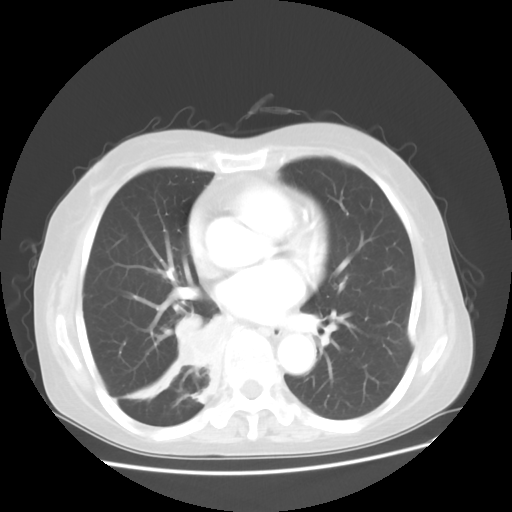
Chest CT, one axial slice. Slice 21 of 48 in the series (ordered by position). 120 kVp. Lung window (W 1500 / L -600 HU). 5 mm slice thickness. 512 × 512 image matrix, field of view 360 × 360 mm. Patient: female, 63 years. Case-level facts recorded for this patient, not image findings: clinical TNM (as recorded): T2 N3 M1b; histopathological grade: G3.
Annotated regions visible in this slice (bounding box drawn by a radiologist):
- lung tumour (recorded histology: small cell carcinoma): bounding box (x1, y1, x2, y2) in pixels: (172, 314, 225, 374)